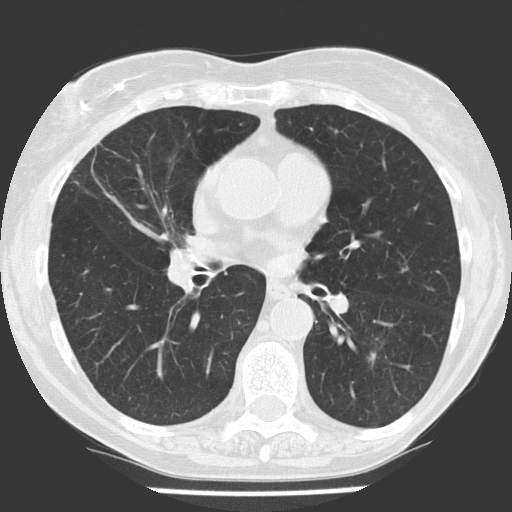
Low-dose screening chest CT, axial slice; baseline screening round; lung window (W 1500 / L -600 HU); lung (sharp) reconstruction kernel (FC51). Female, age 68 years at enrolment. Former smoker at enrolment.
• Expert-annotated lung lesion, bounding box (x1, y1, x2, y2) in pixels: (343, 324, 398, 379).
• No non-calcified nodule or mass ≥4 mm was recorded by the screening reader at this exam.
• Later outcome: lung cancer diagnosed 895 days after this screen (after the third annual screen) — non-small cell carcinoma, left lower lobe, poorly differentiated (G3), stage IA (AJCC 6th edition), 10 mm at pathology.